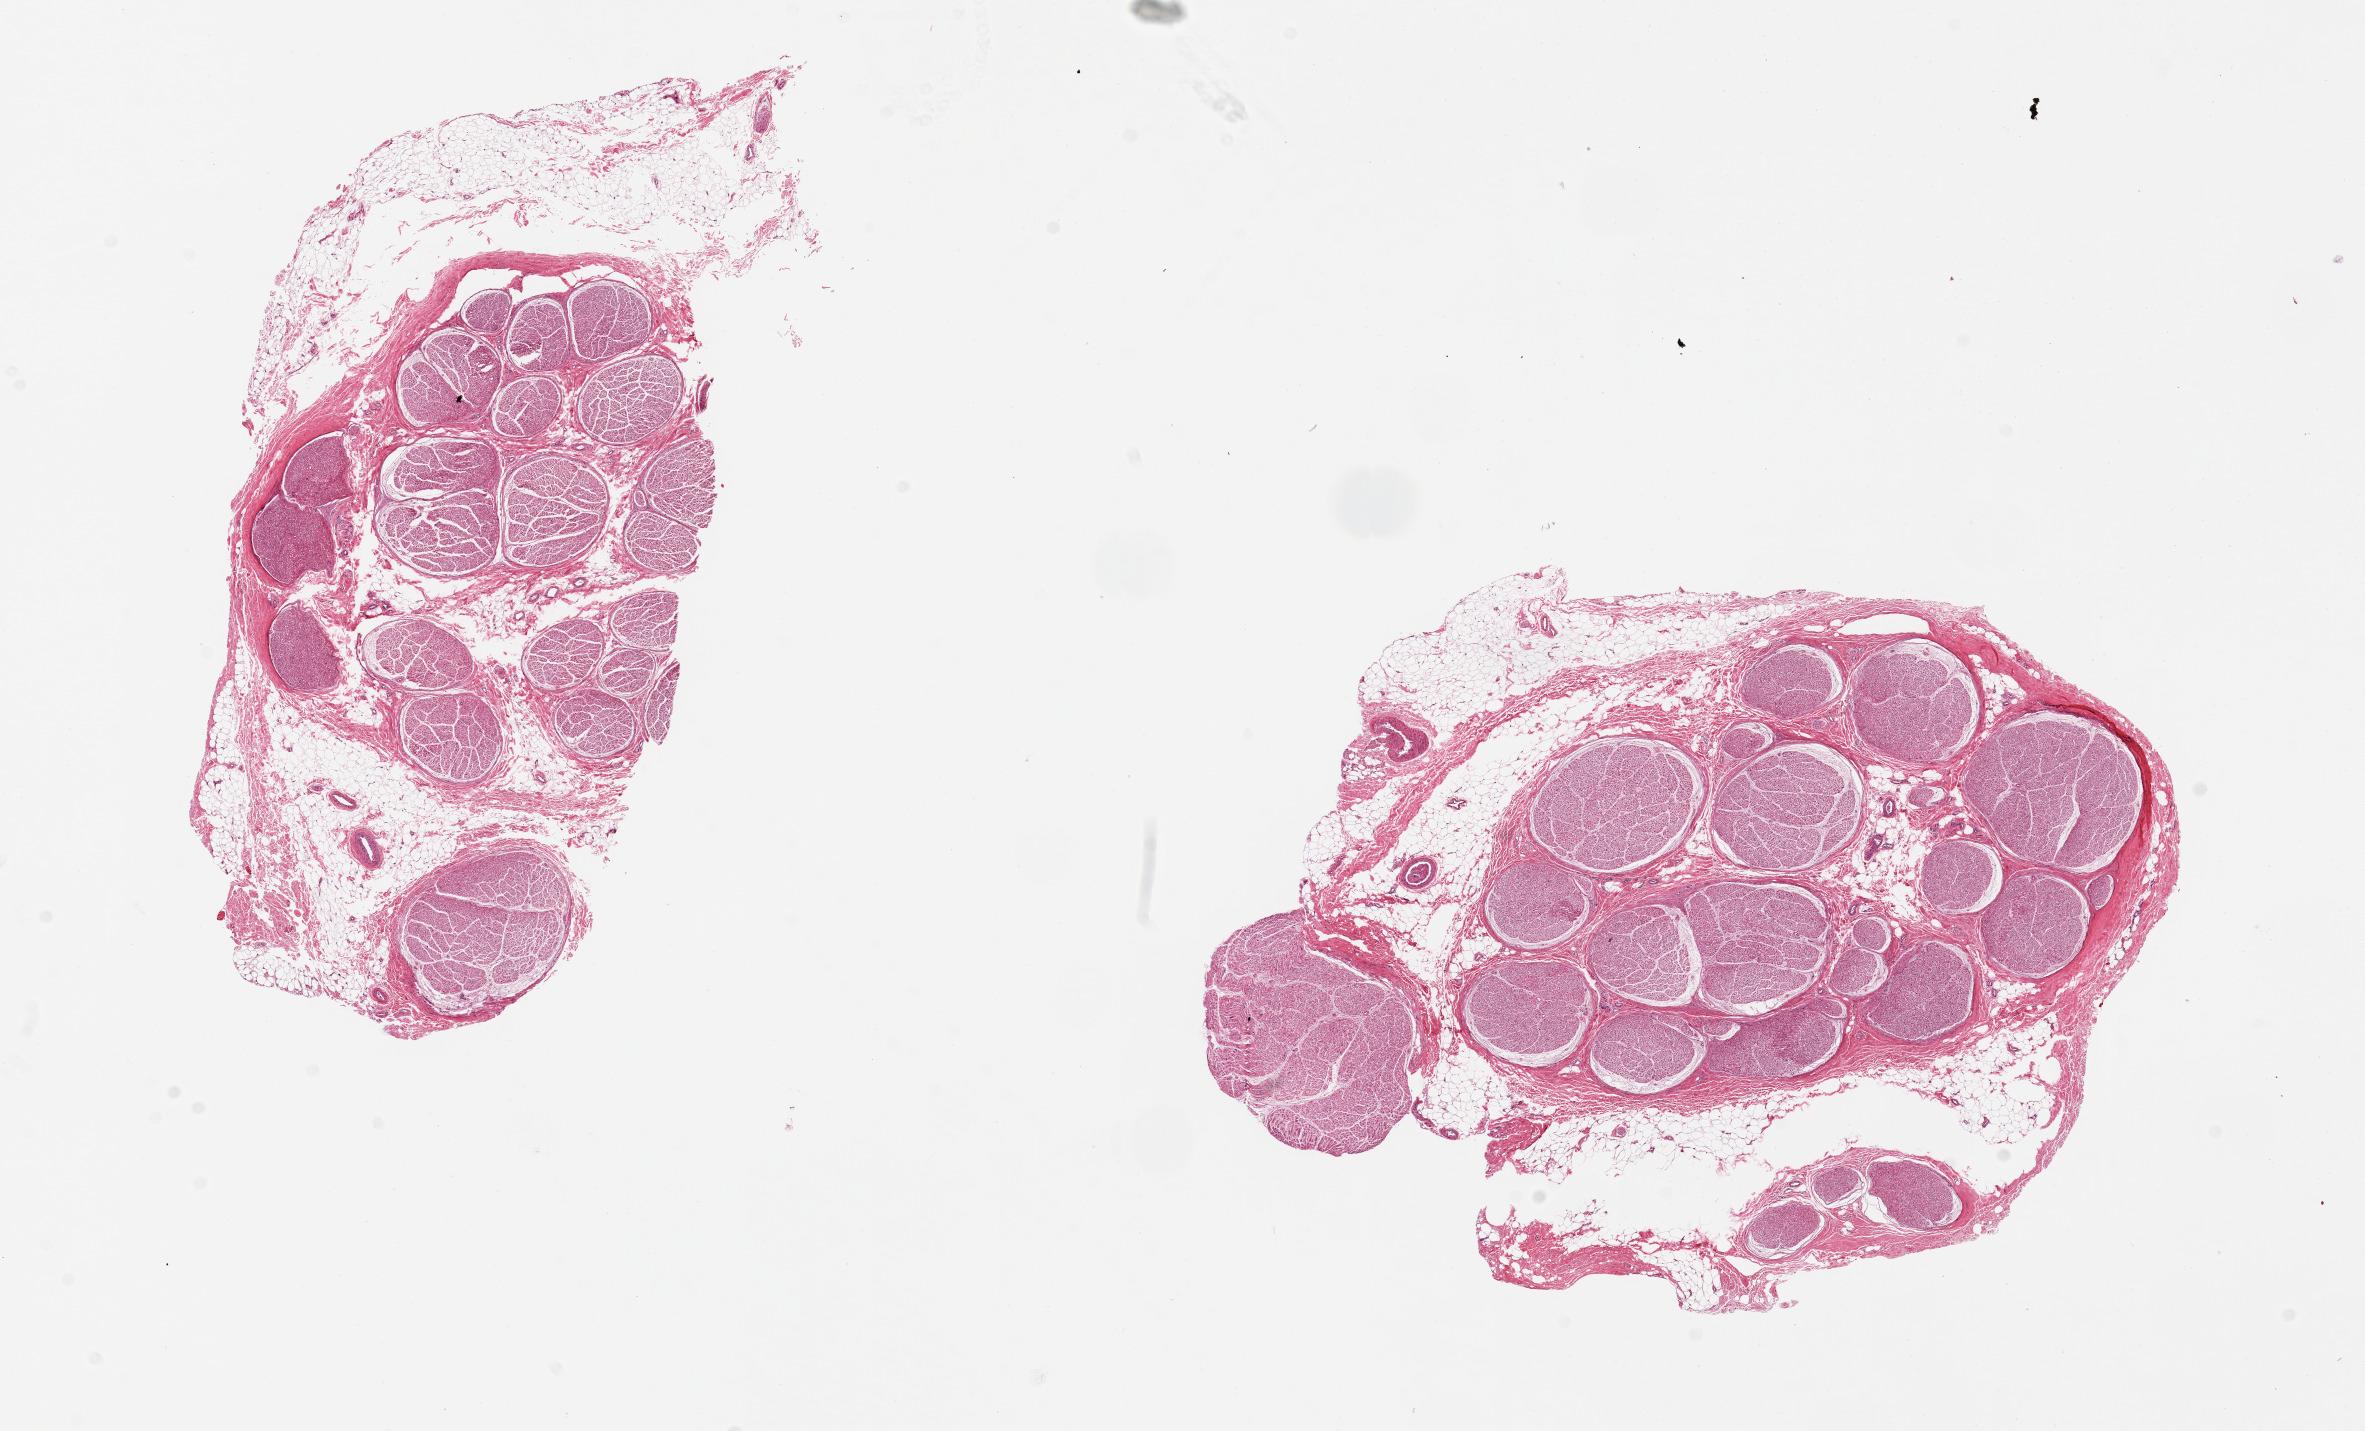
Hematoxylin and eosin (H&E) whole-slide image, brightfield, shown as a low-resolution overview of the whole scanned area (about 18.7 x 11.3 mm, slide scanned at 20x), PAXgene-fixed, paraffin-embedded tissue, section of tibial nerve (target tissue), donor tissue sample. Donor: female.
* reviewer comment on this tissue sample: 2 pieces, 8x4.5 & 8x6mm; discontinous adherent rim of fat, up to ~1mm thick